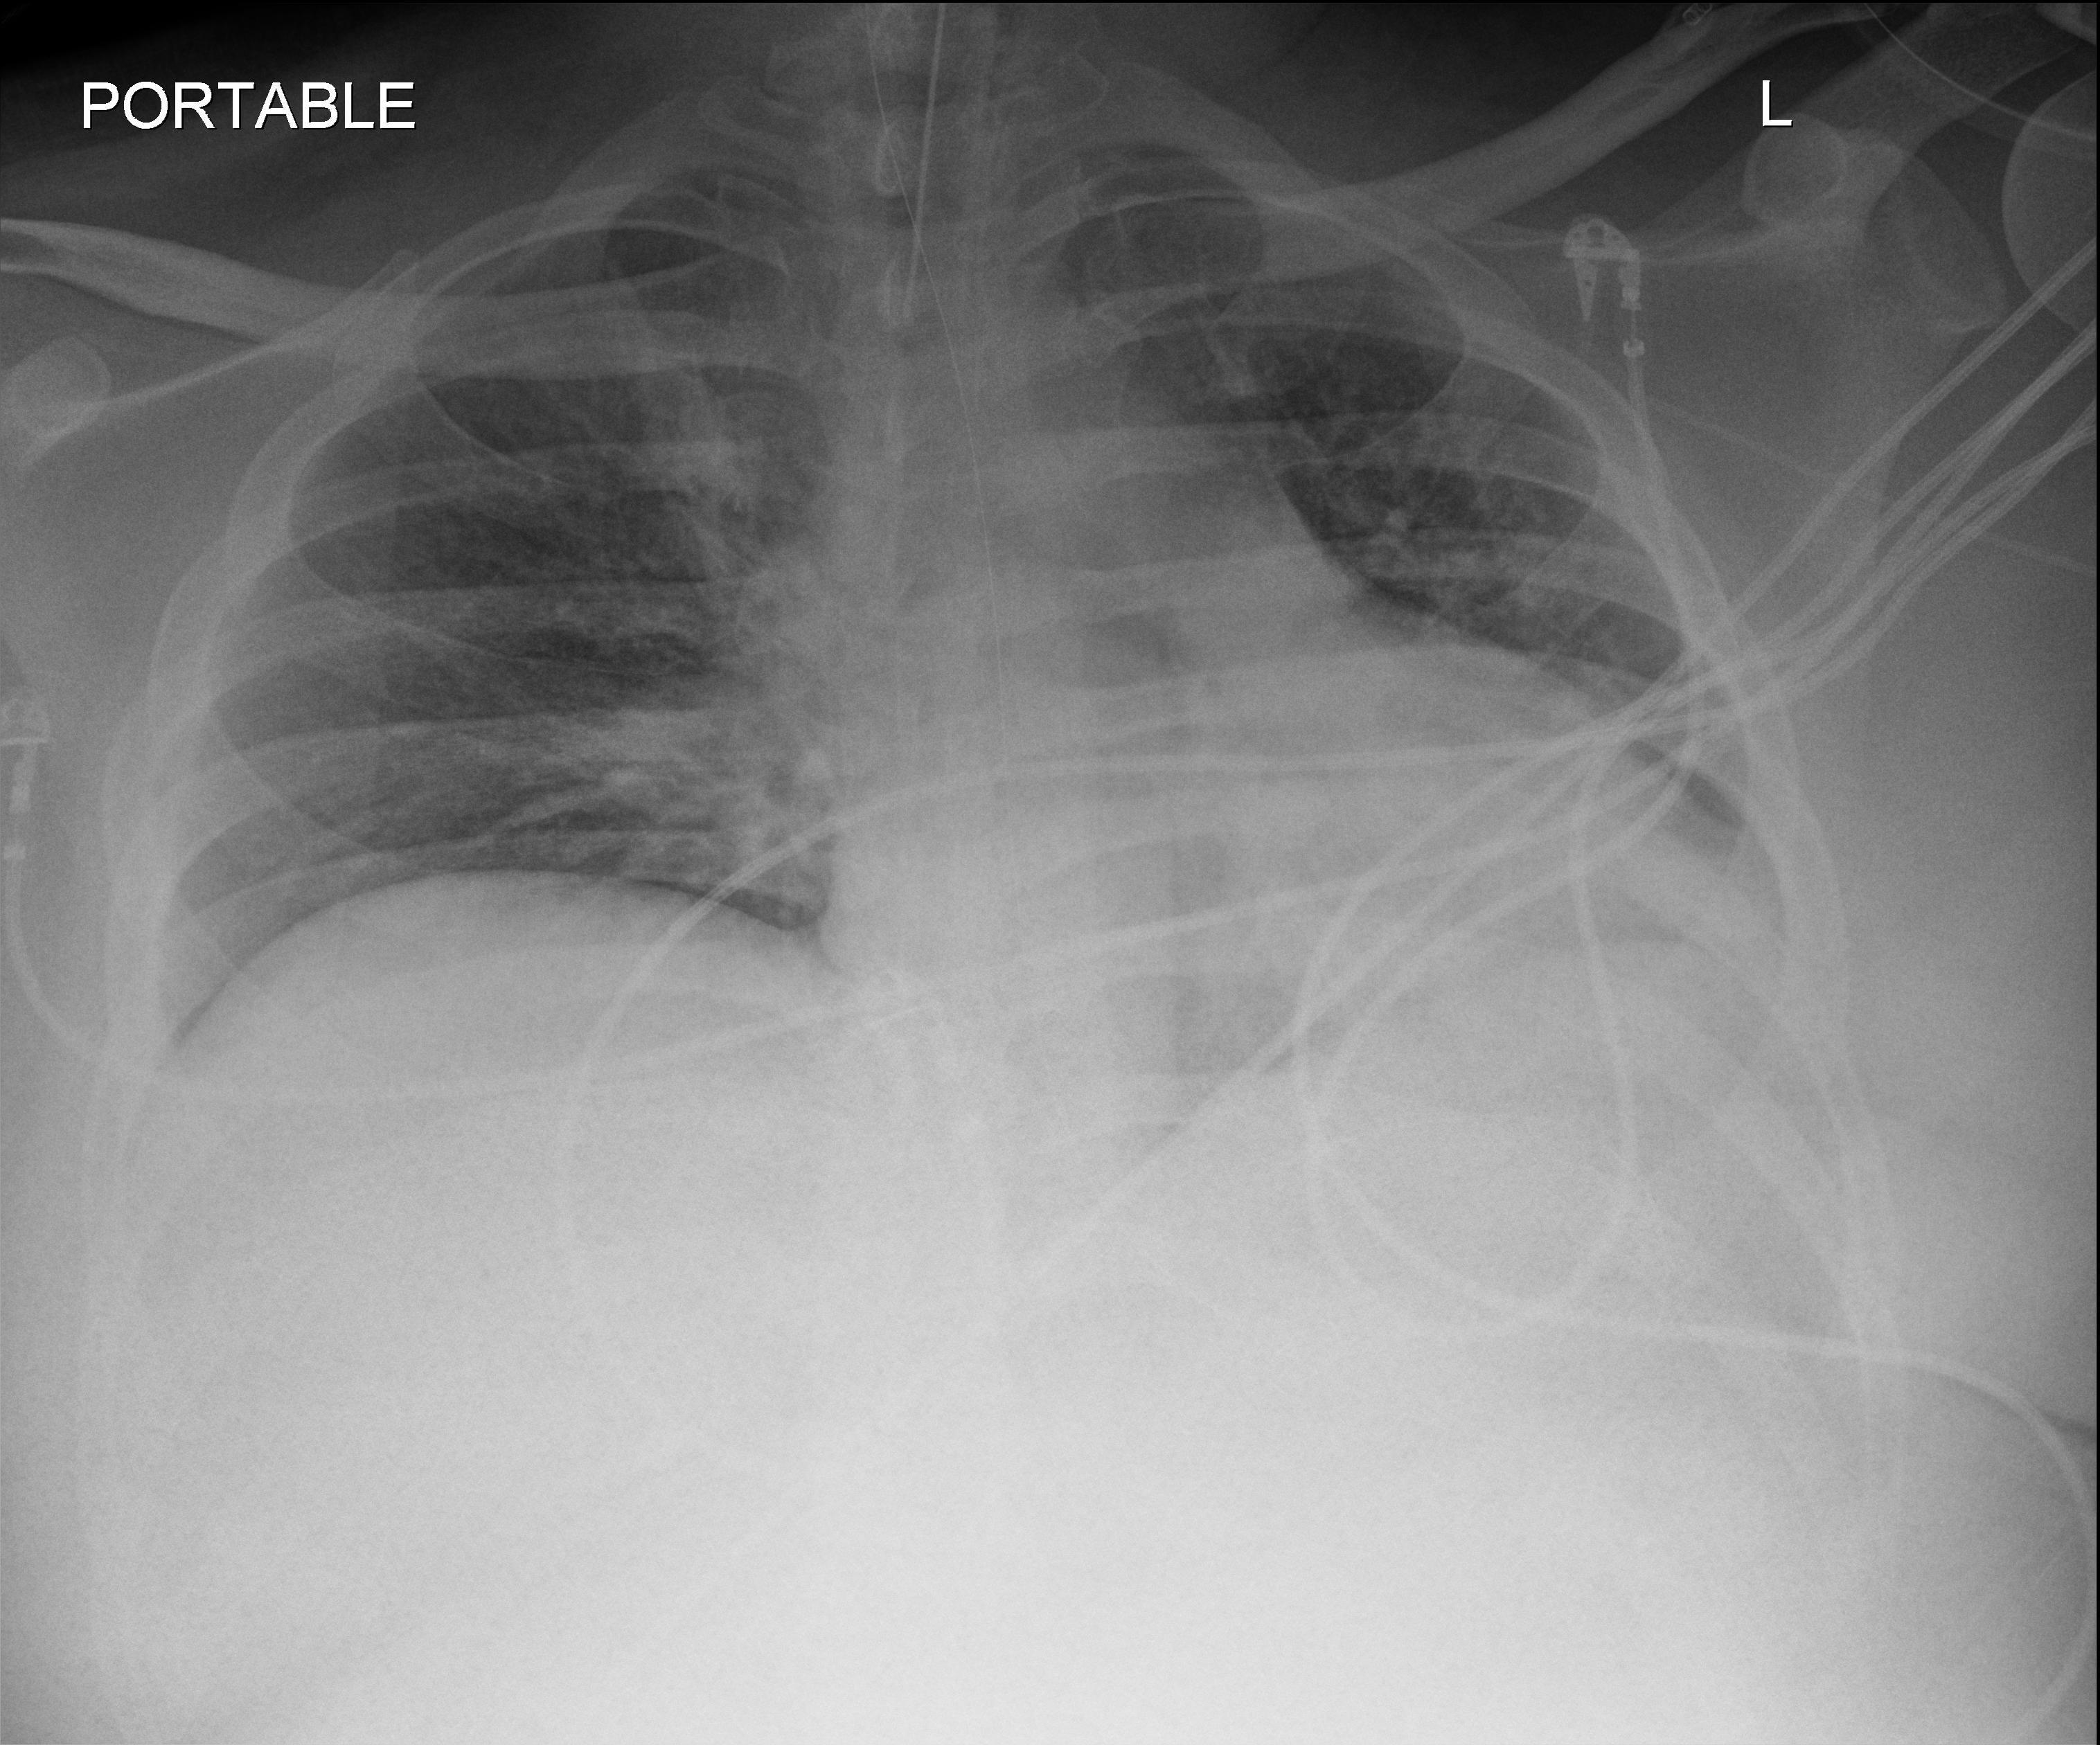
Bedside chest radiograph (digital radiography); anteroposterior (AP) projection. Patient hospitalised with COVID-19; male, aged 18–59 years.
From the hospital-stay record, not from the radiograph (when in the stay this image was taken is not recorded):
- admitted to intensive care during this hospital stay: yes
- mechanically ventilated during this hospital stay: yes